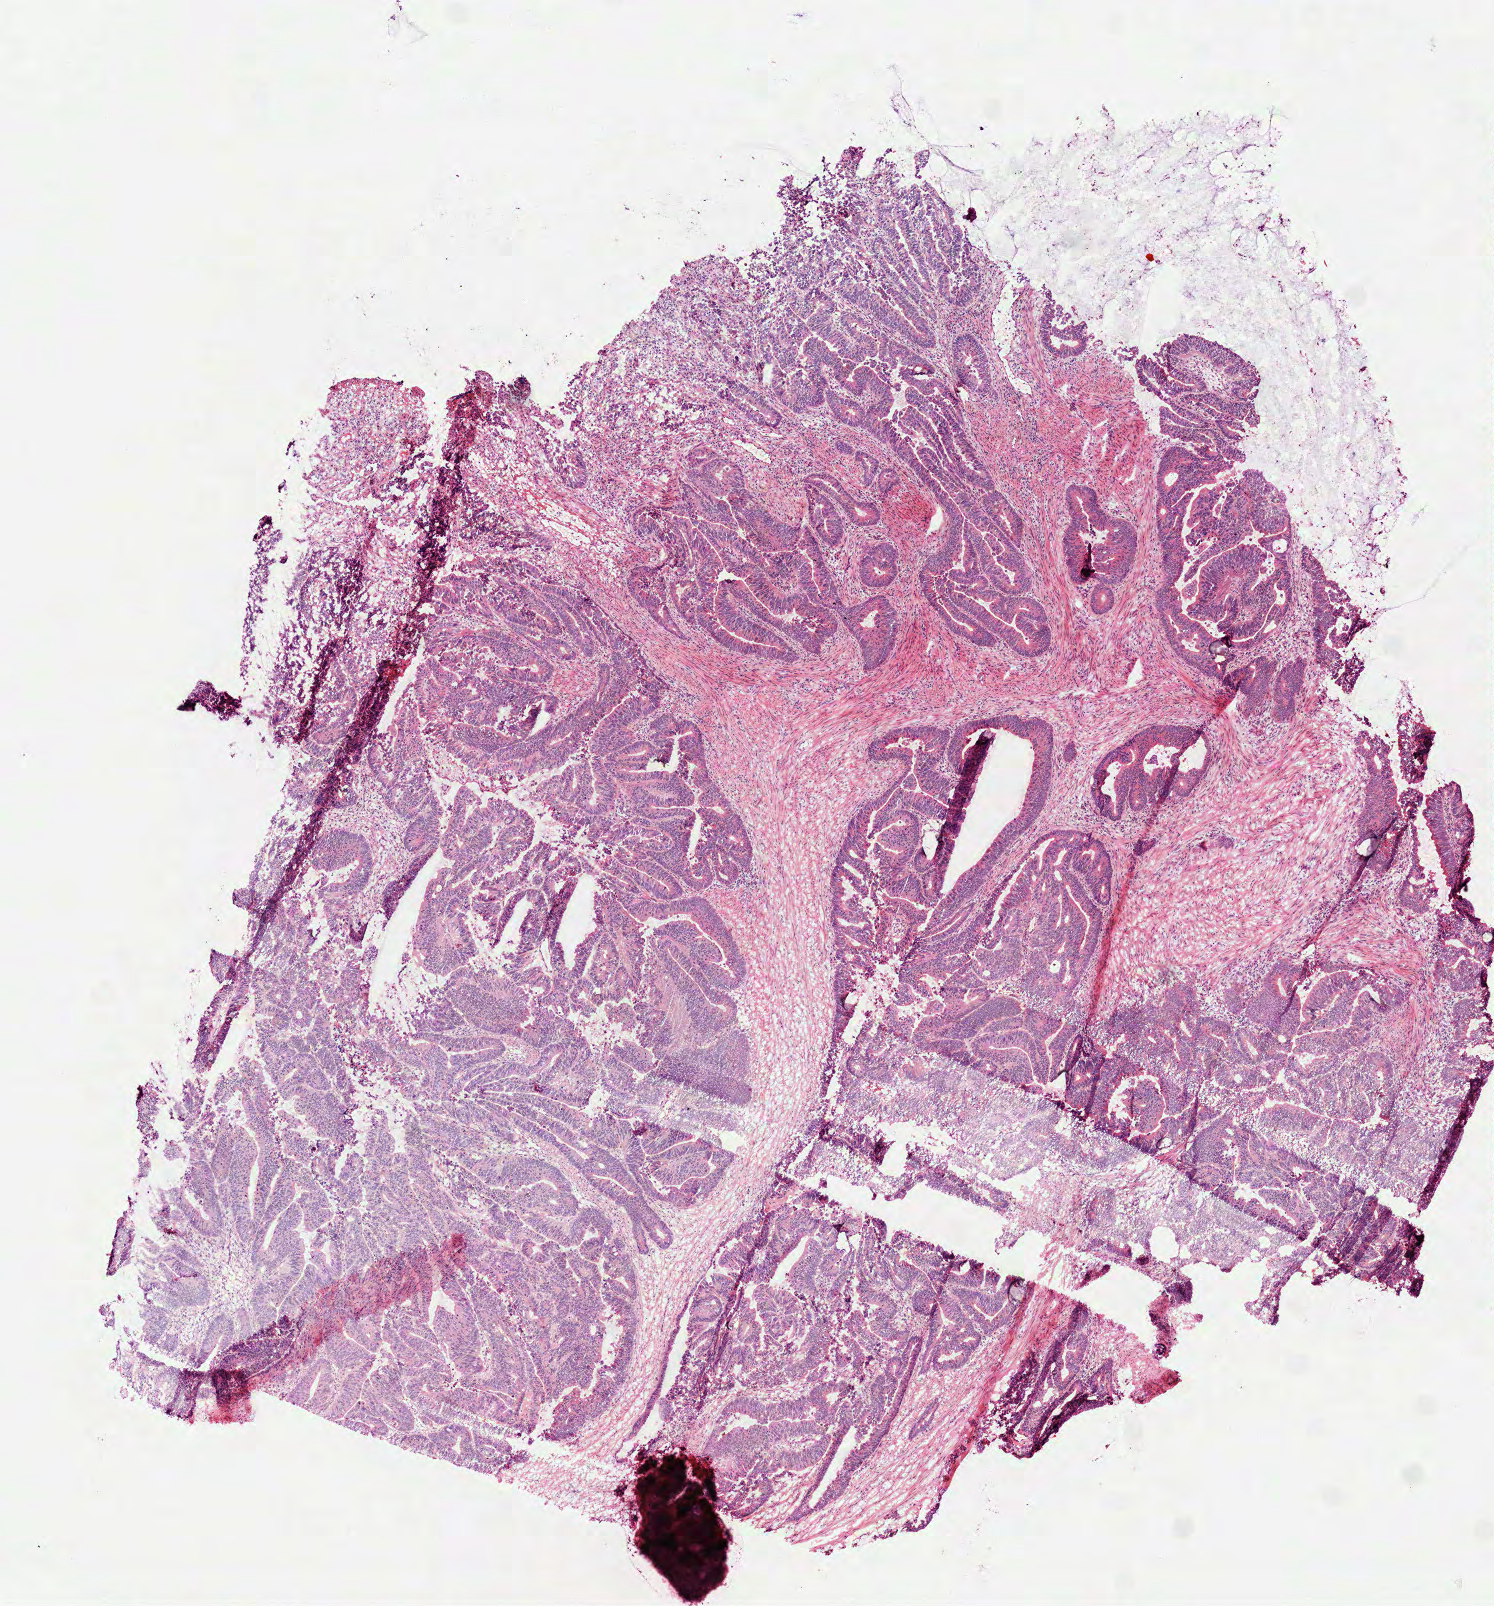
Hematoxylin and eosin (H&E) stained whole-slide image, a low-resolution overview of the entire scanned area, about 6.0 x 6.5 mm (acquisition: 40x scan); frozen section from the top of the tissue portion; sample: primary tumour, rectum. Male, age 58 years at initial diagnosis. Composition of this section per pathologist review: tumour cells 70%, tumour nuclei 80%, normal cells 0%, stromal cells 15%, necrosis 15%.
Histologic diagnosis: Tubular adenocarcinoma. Lymph nodes positive (case pathology): 7 of 13 examined. AJCC pathologic stage: IV (7th edition).